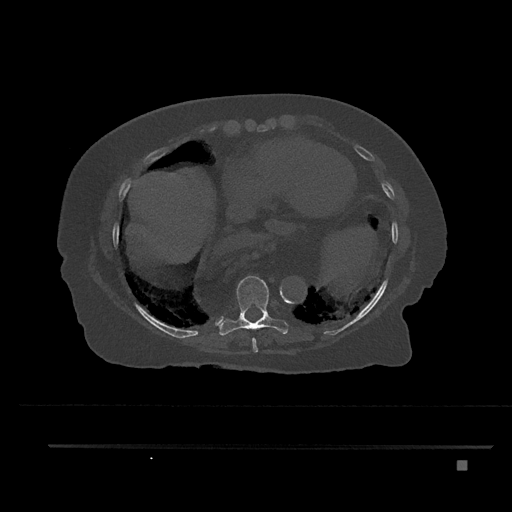
CT including the spine, one axial slice. Slice 404 of 797 in the series (ordered by position). Reconstruction kernel Br40s/3. Bone window (W 1800 / L 400 HU). 0.5 mm slice thickness. 512 × 512 image matrix. Female patient, age 76 years. From the clinical record (not read from this slice): primary cancer: lung.
Outlined on this slice (semi-automatic segmentation, software-assisted and operator-edited):
- T8 vertebra: bounding box <252,337,258,353> (left, top, right, bottom; pixels)
- T9 vertebra: <216,276,288,336>